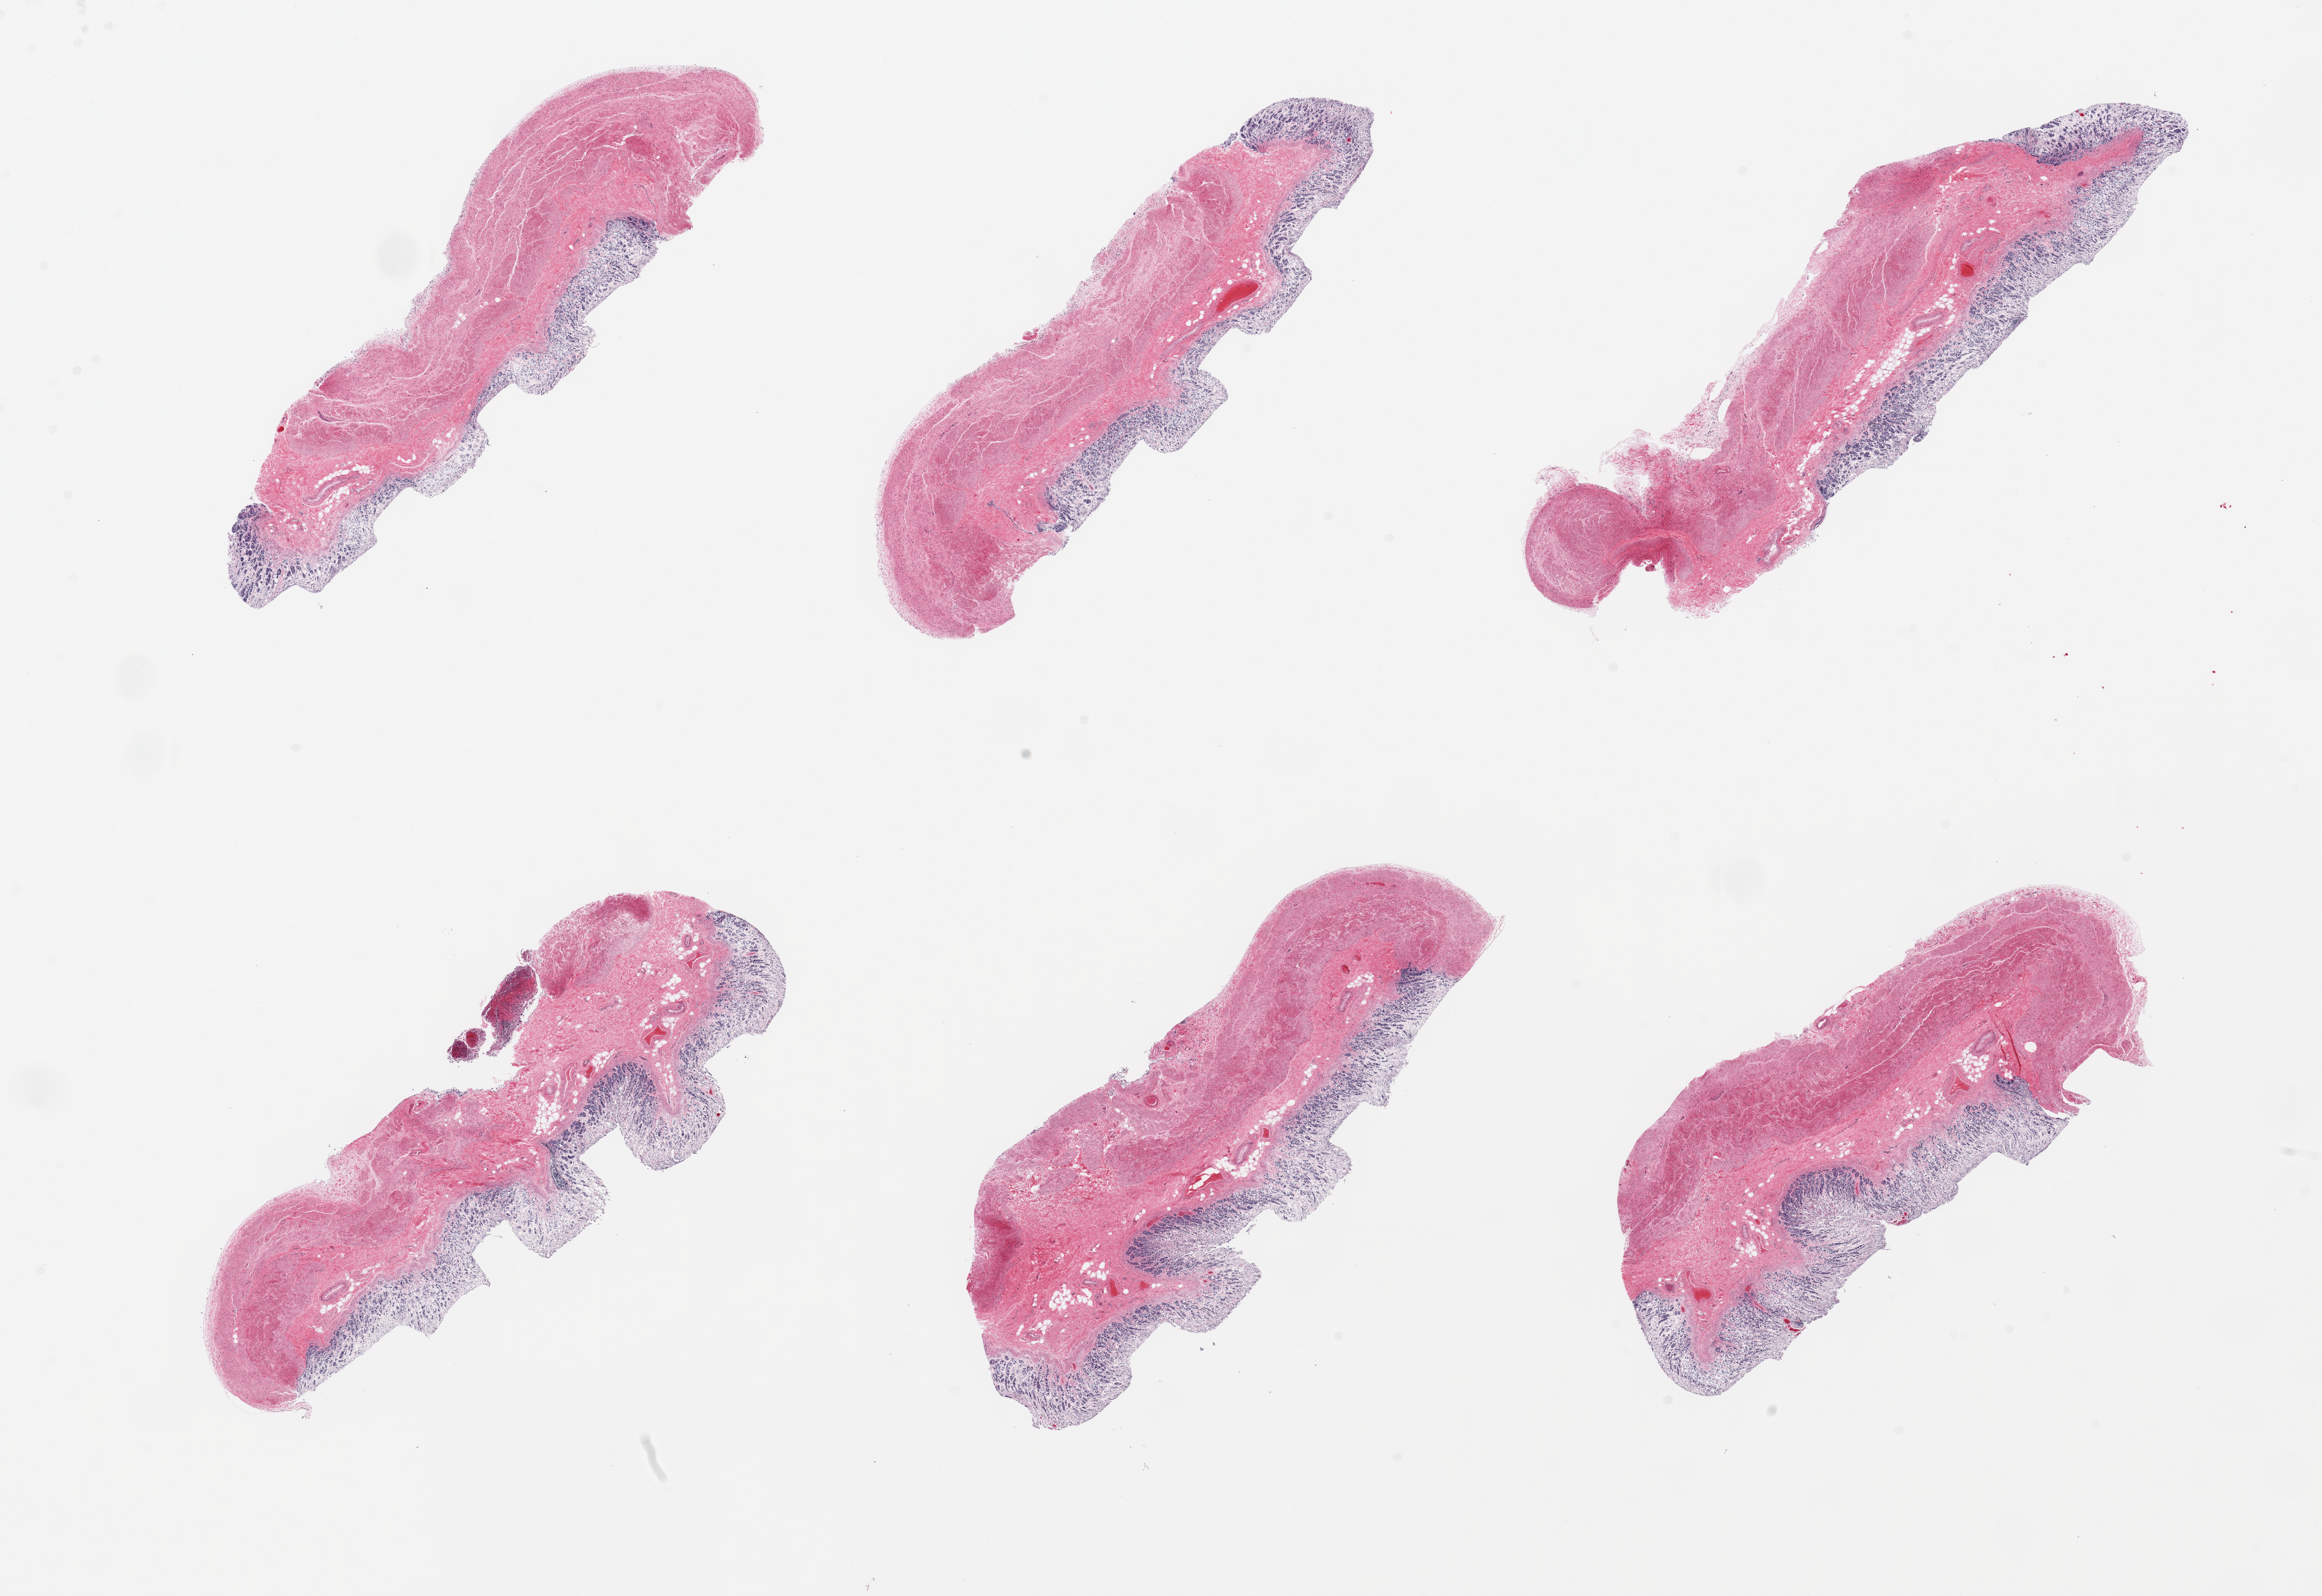
Whole-slide image, H&E stain — whole scanned area (about 26.6 x 18.3 mm, from a 20x scan) shown as a low-resolution overview; PAXgene-fixed paraffin-embedded (PFPE) section; sampled site (target tissue): stomach; tissue donor sample. Female donor.
Pathologist's review note for this sample: 6 pieces; full thickness sections, moderate to severe autolysis.